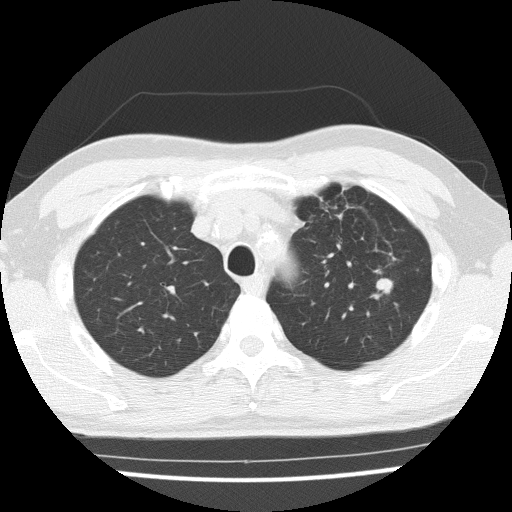
Axial slice from a low-dose chest CT screening exam; third annual screen; lung window (W 1500 / L -600 HU); lung (sharp) reconstruction kernel (FC51); slice 38 of 154 in the series; 512 × 512 image matrix. Male, age 65 years at enrolment. Current smoker at enrolment.
Expert reader's lesion annotation, bounding box (x1, y1, x2, y2) in pixels: (354, 269, 407, 314). Screening reader's record for this exam (one nodule recorded; not confirmed to be the boxed lesion): non-calcified nodule or mass ≥4 mm, left upper lobe, 16 × 15 mm, poorly defined margins, soft tissue attenuation, pre-existing on the prior screen: yes; interval growth: yes. Official screen result: positive, other. Lung cancer was diagnosed 42 days after this screen: squamous cell carcinoma, NOS, left upper lobe, moderately differentiated (G2), stage IA (AJCC 6th edition), 25 mm at pathology.